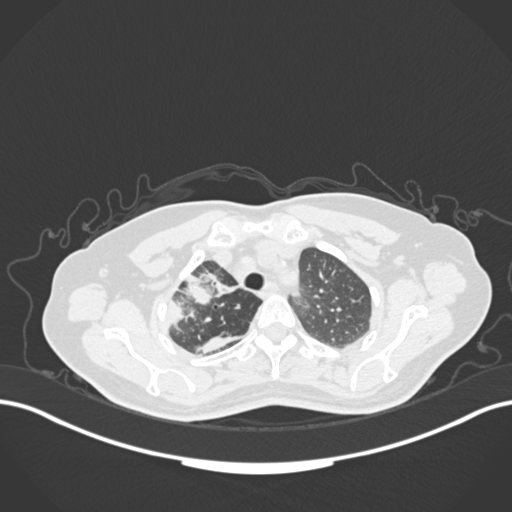
Chest CT, one axial slice. Position 133 of 177 along the scan axis. Lung window (W 1500 / L -600 HU). 1 mm slice thickness. 512 × 512 image matrix, field of view 400 × 400 mm. Patient: female, 60 years. From the clinical record (not read from this slice): clinical TNM (as recorded): T3 N1 M1.
Outlined on this slice (rectangle marked by the reading radiologist):
- lung tumour (recorded histology: adenocarcinoma): bounding box [x1, y1, x2, y2] px = [157, 260, 240, 335]